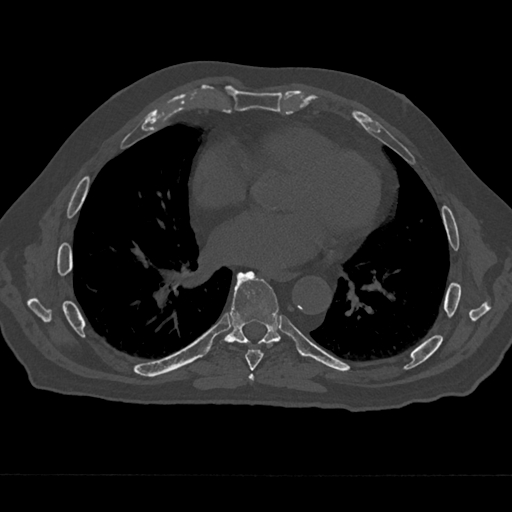
CT including the spine, one axial slice. Slice 341 of 797 in the series (ordered by position). Bone window (W 1800 / L 400 HU). 0.5 mm slice thickness. 512 × 512 image matrix, field of view 377 × 377 mm. Male patient, age 75 years. Case-level facts recorded for this patient, not image findings: primary cancer: renal.
Outlined on this slice (semi-automatically segmented with operator editing):
- T6 vertebra: bounding box (x1, y1, x2, y2) in pixels: (249, 374, 254, 382)
- T7 vertebra: (238, 272, 273, 371)
- T8 vertebra: (215, 271, 281, 353)